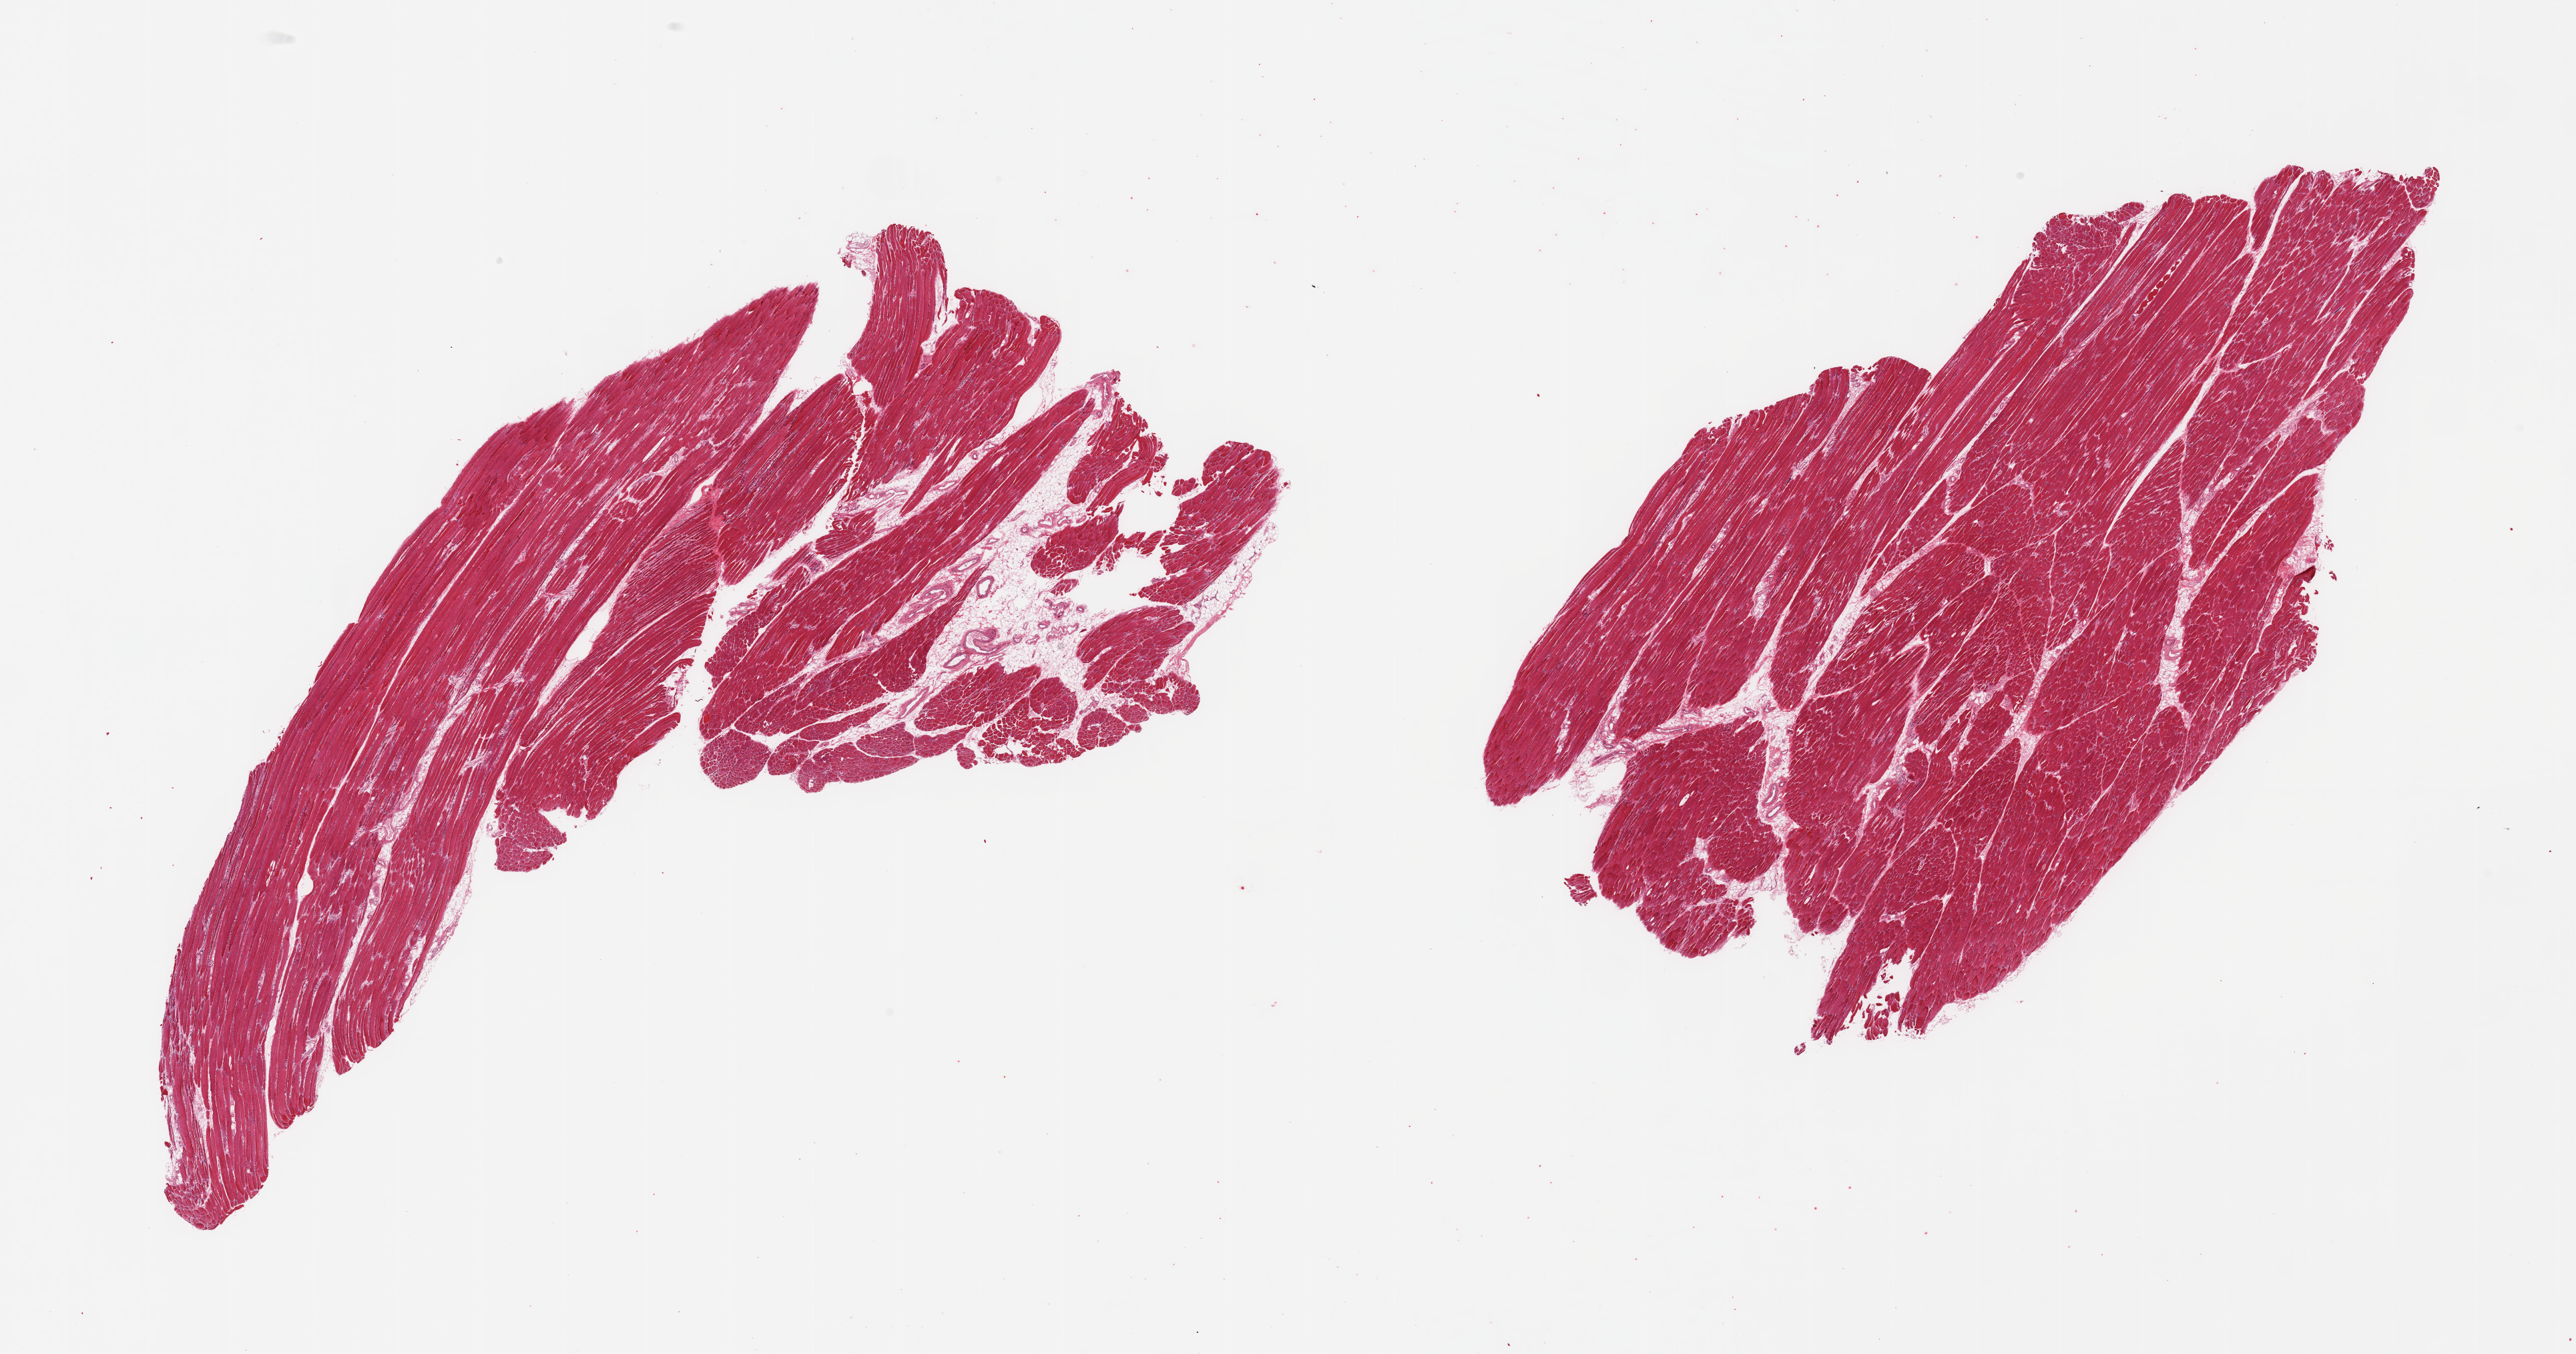
Whole-slide image, hematoxylin and eosin (H&E) stain — low-resolution overview of the scanned area, about 30.5 x 16.0 mm. PAXgene-fixed, paraffin-embedded tissue. Section of skeletal muscle (target tissue). Tissue donor sample. Donor: female.
Review note (as recorded): 2 pieces; scattered atrophic fibers; 10% internal fat in 1 piece.